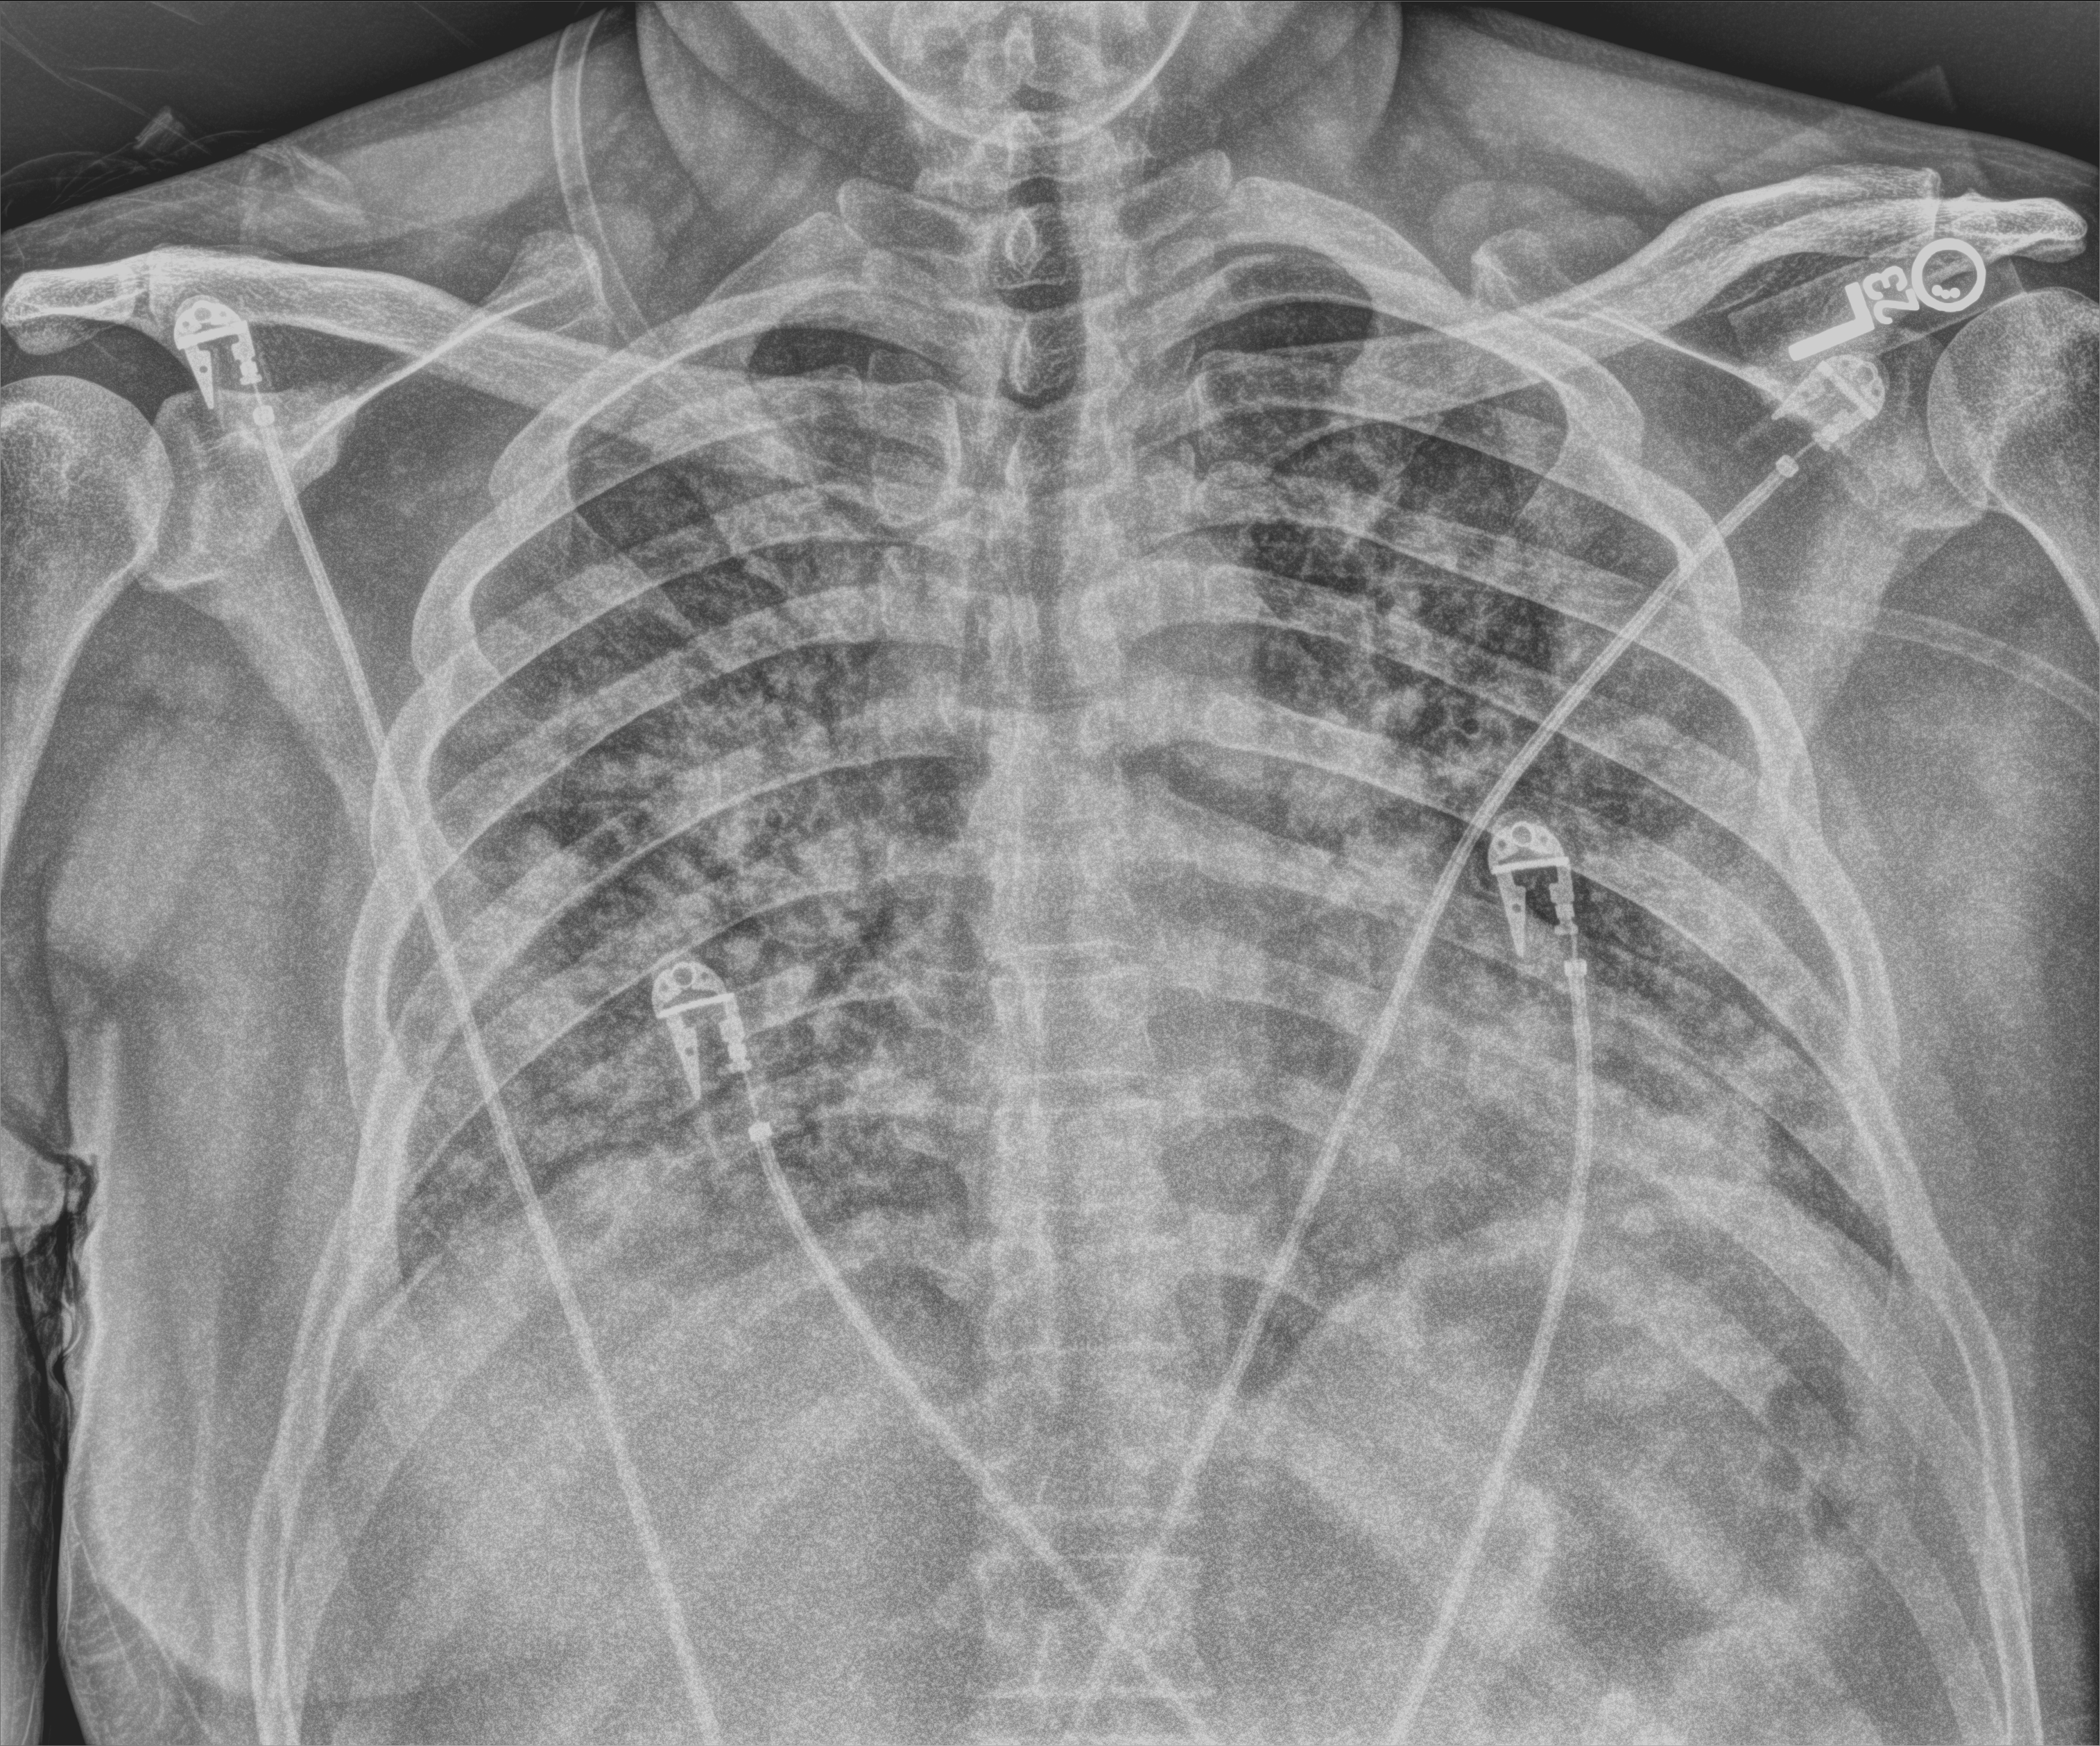
Portable chest radiograph; anteroposterior (AP) projection. Male patient hospitalised with COVID-19, age 18–59 years.
Admission-level facts for this patient (not findings on this image; timing relative to this image not recorded):
- mechanically ventilated during this hospital stay: yes